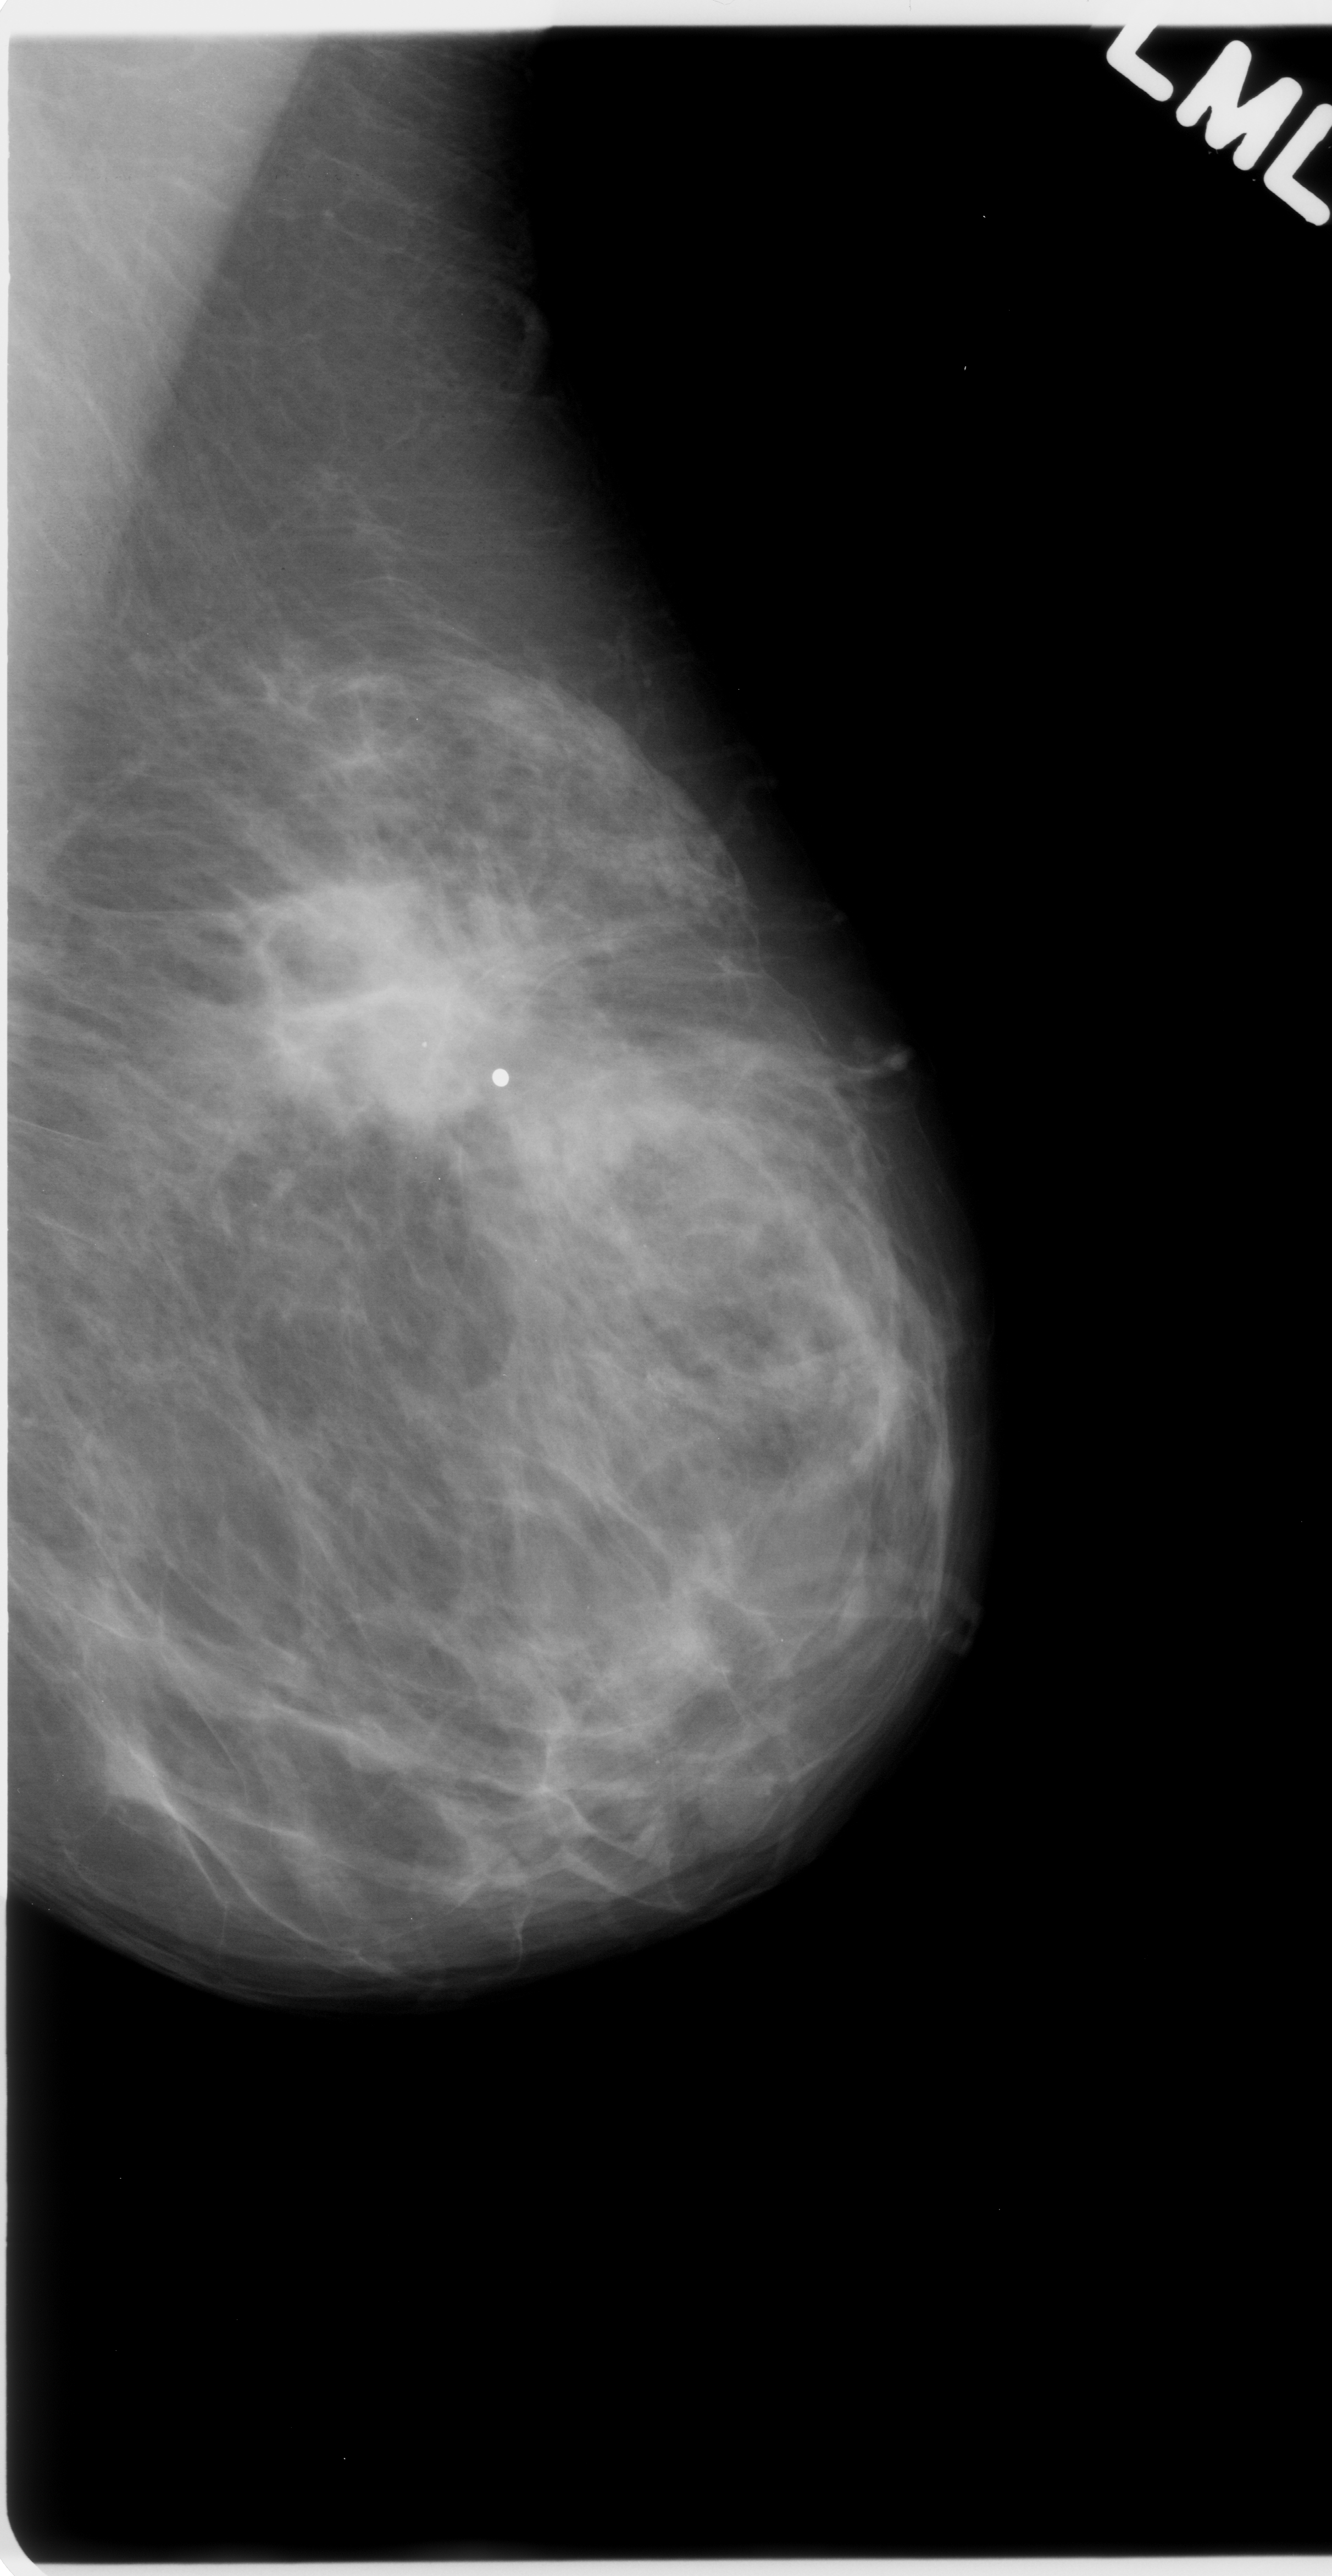
Mammogram (digitized film); left breast; MLO view; 1332 × 2576 image matrix.
Expert-marked regions of interest on this film, with their recorded descriptors:
- mass, shape irregular, margins ill defined; BI-RADS assessment category 5; subtlety rating 5 on a 1 (subtle) to 5 (obvious) scale; pathology result (as recorded, not read from the image): malignant: bounding box <222,868,592,1183> (left, top, right, bottom; pixels)